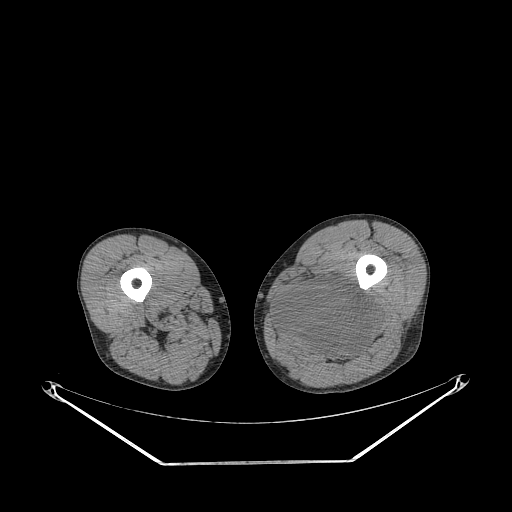
CT of an extremity soft-tissue mass (from a PET/CT study), one axial slice. Slice 235 of 267 in the series (ordered by position). Reconstruction kernel STANDARD. 140 kVp. Soft-tissue window (W 400 / L 40 HU). 3.75 mm slice thickness. 512 × 512 image matrix. Male patient. Case-level facts recorded for this patient, not image findings: histological type: undifferentiated pleomorphic liposarcoma; grade: high; site of the primary tumour: left thigh.
Structures marked on this image (expert contour drawn on MRI and transferred to this co-registered scan by the dataset authors):
- gross tumour volume including surrounding oedema: bounding box [x1, y1, x2, y2] px = [276, 279, 380, 362]
- gross tumour volume (mass): [276, 279, 380, 360]